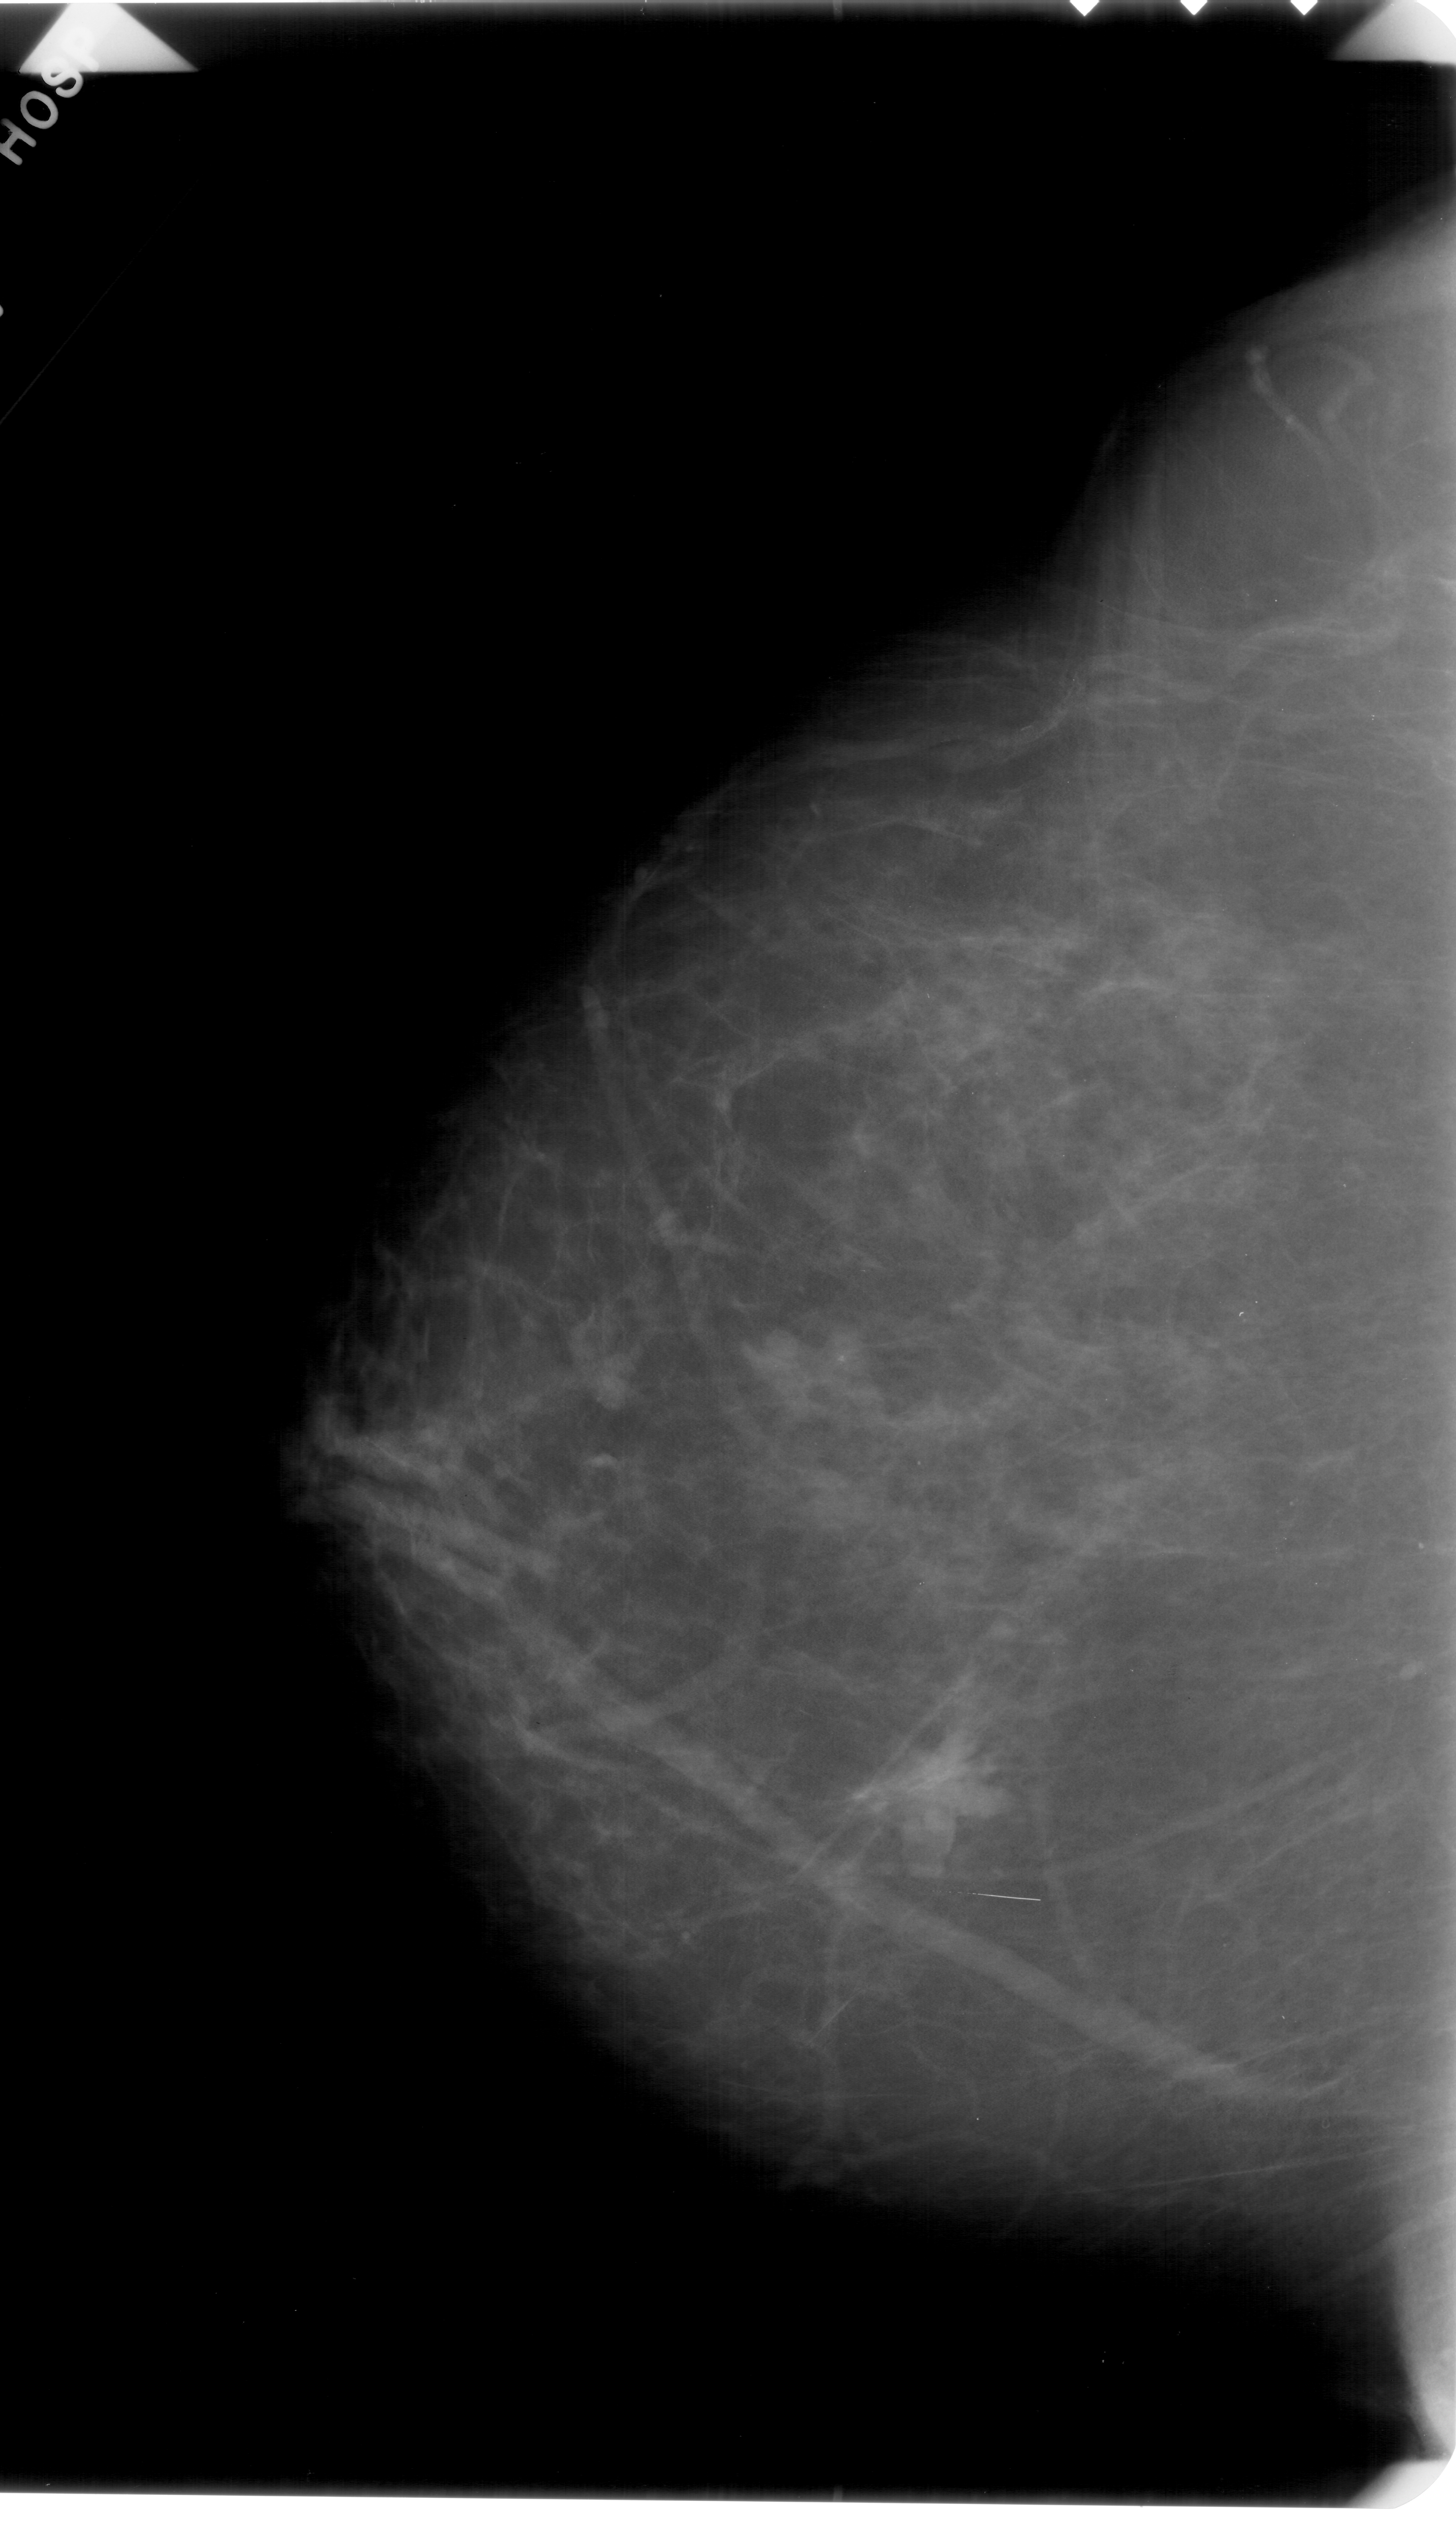
Digitized screen-film mammogram. Left breast. Craniocaudal (CC) view. BI-RADS breast density category 2 (scale 1–4). 1456 × 2545 image matrix.
Expert-marked regions of interest on this image (one box per marked abnormality):
- mass, shape irregular, margins ill defined; BI-RADS assessment category 4; subtlety rating 4 on a 1 (subtle) to 5 (obvious) scale; pathology result (as recorded, not read from the image): malignant: box from (x=874, y=1732) to (x=994, y=1851) px